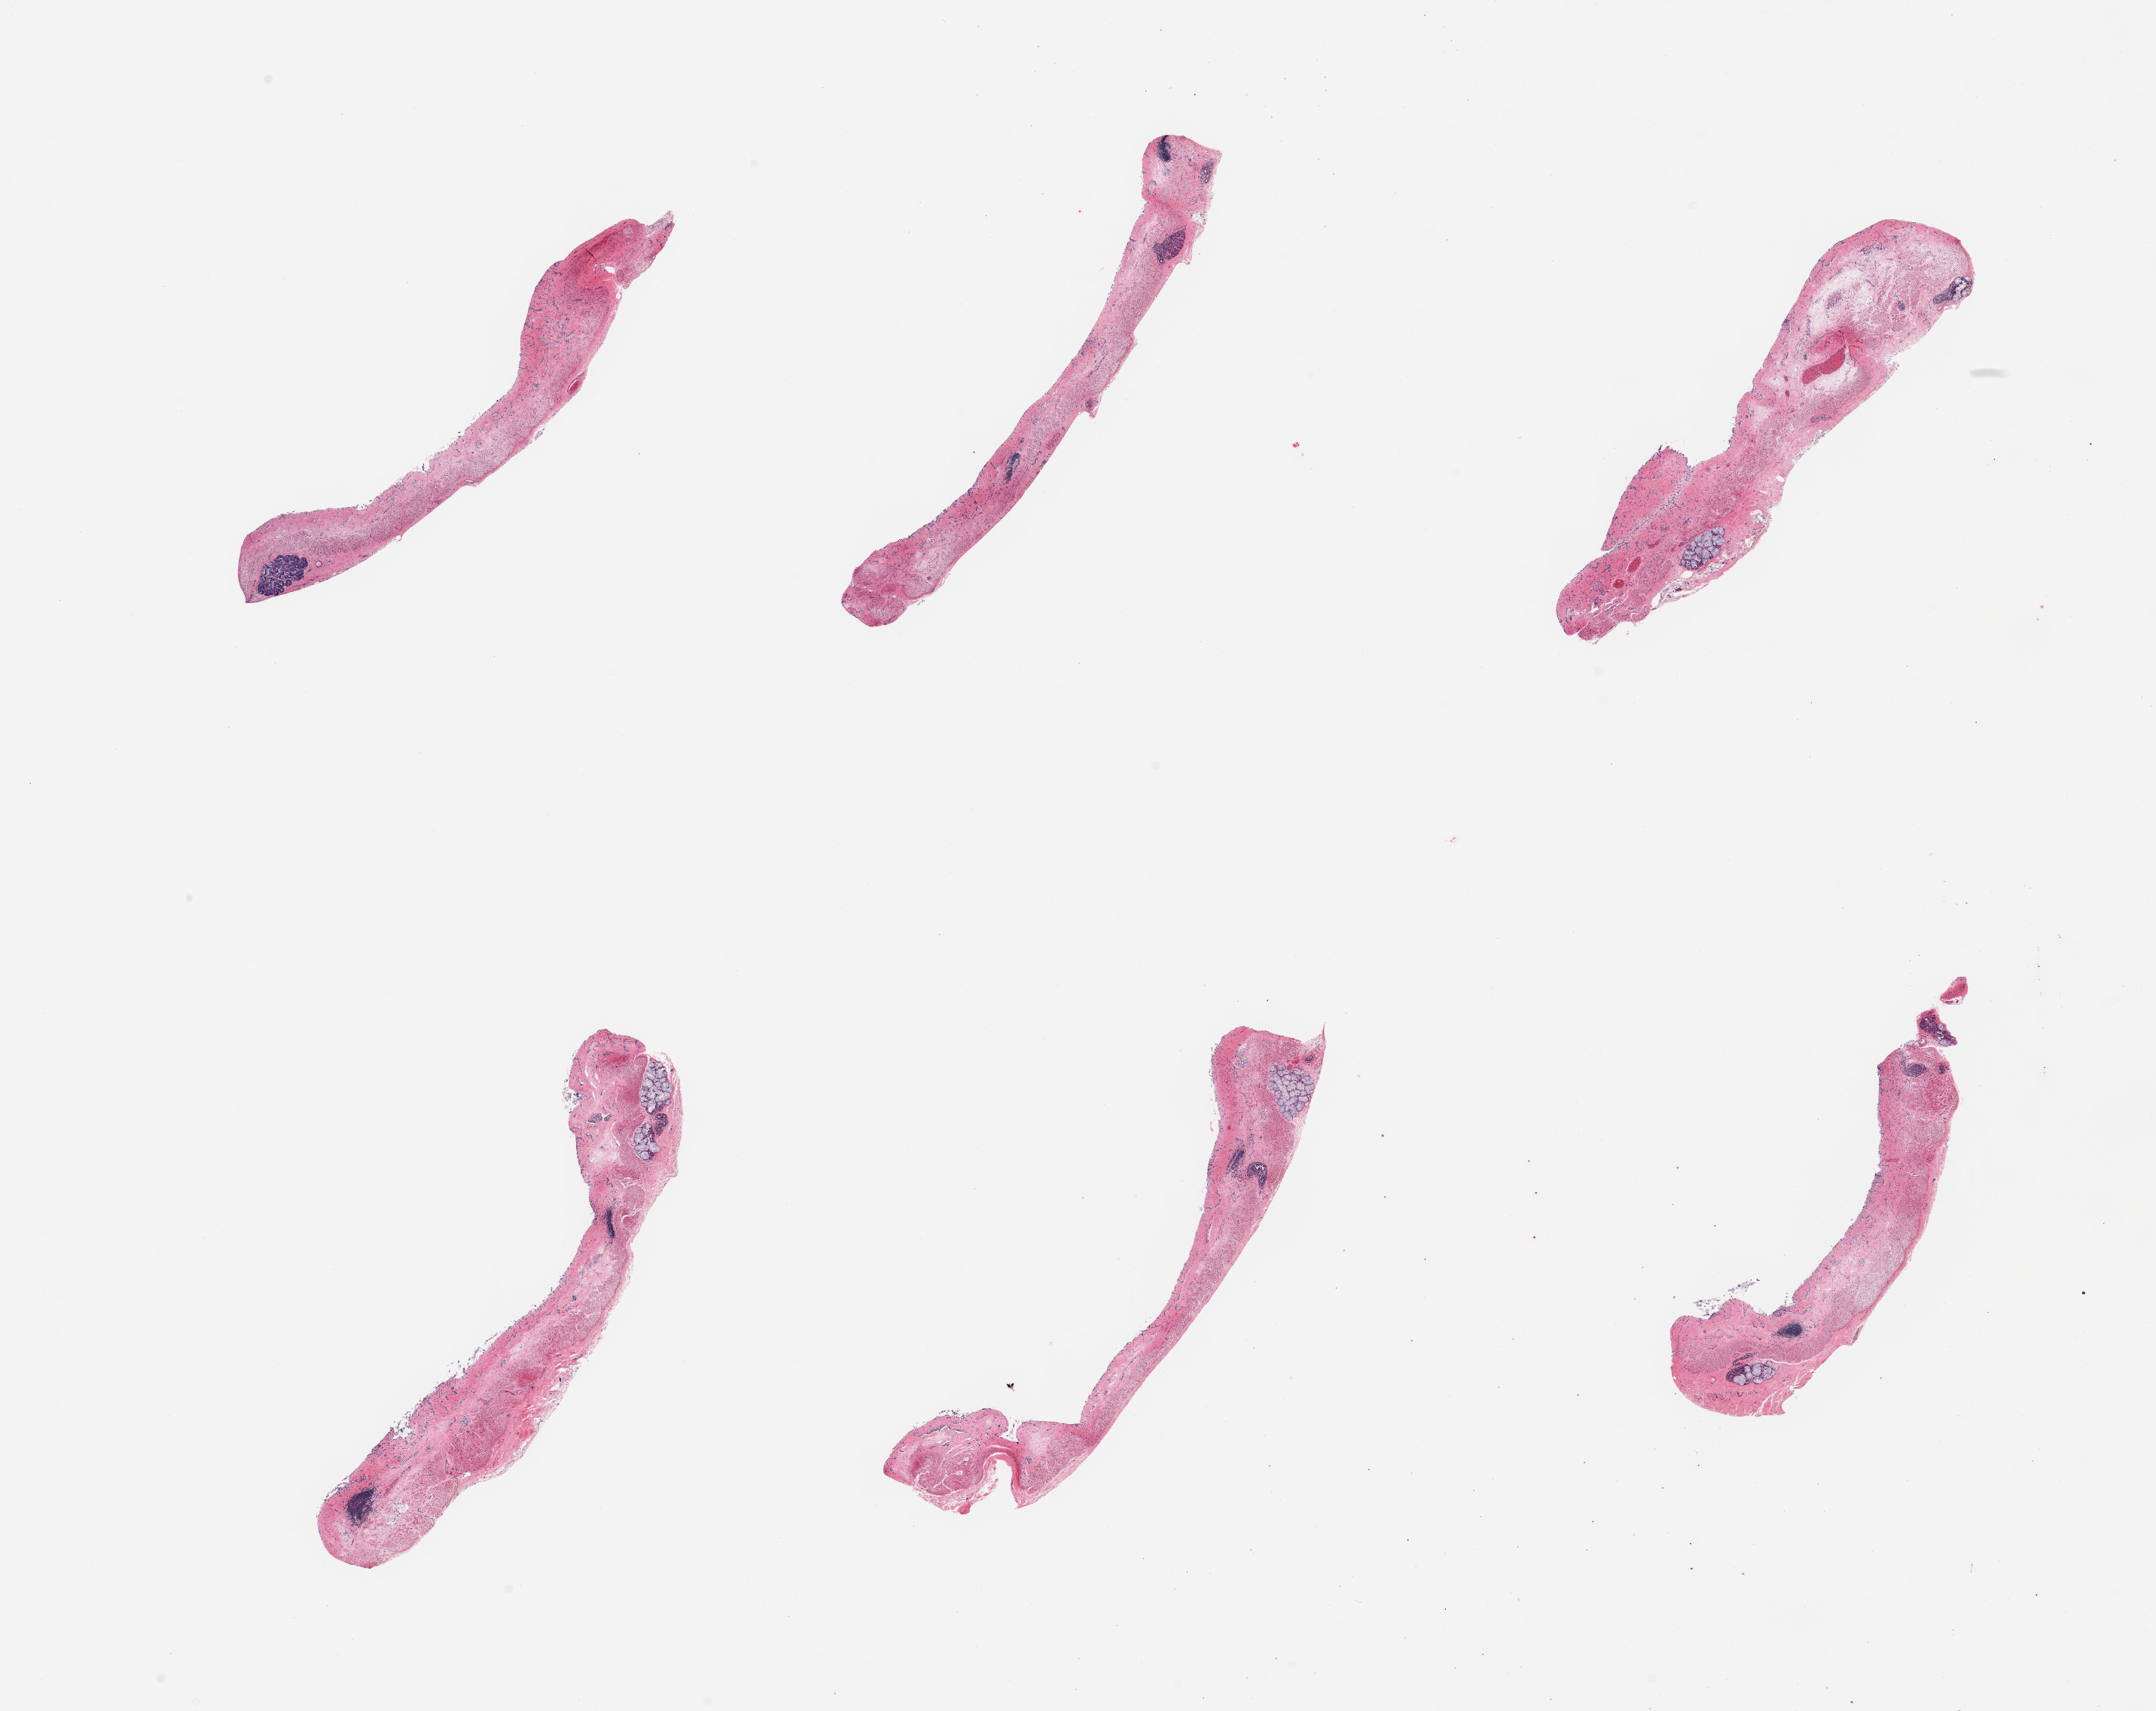
Digitized H&E-stained section, brightfield, a low-resolution overview of the entire scanned area, about 22.6 x 18.0 mm; PAXgene-fixed paraffin-embedded (PFPE) section; sampled site (target tissue): esophageal mucous membrane; tissue donor sample.
- review note (as recorded): 6 pieces; sloughed & autolyzed mucosa